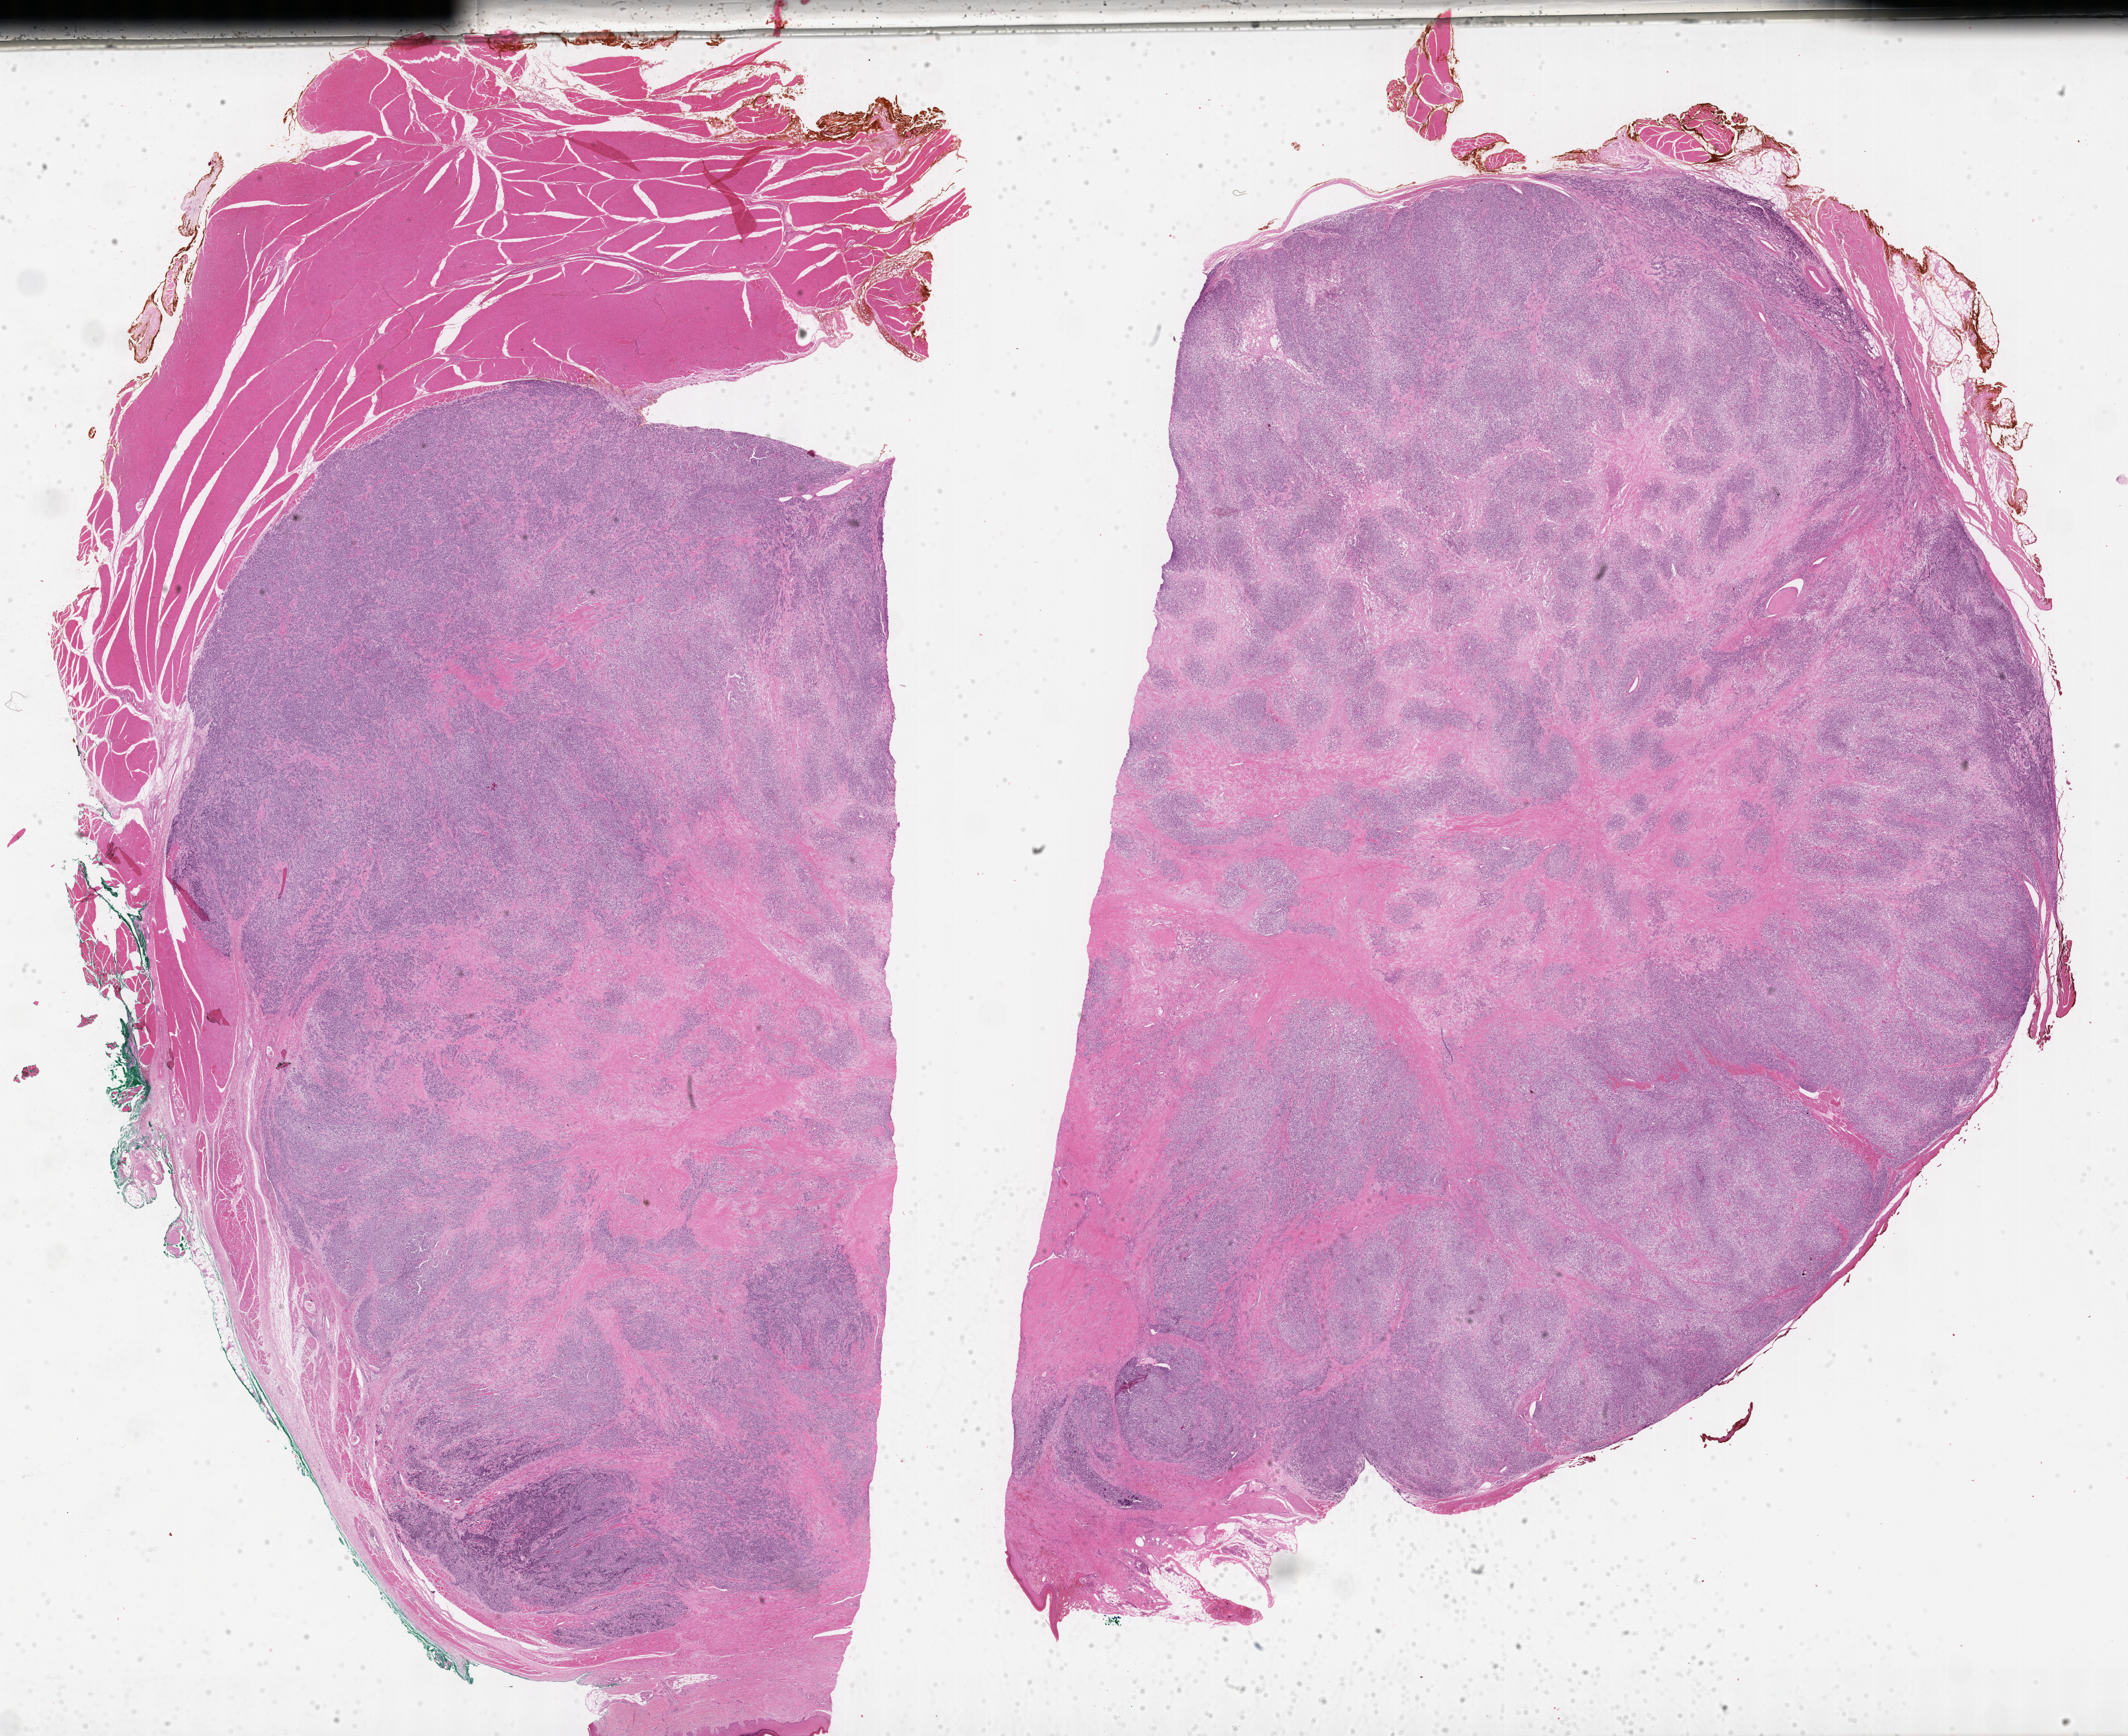
Whole-slide image, haematoxylin and eosin stain of tumor tissue, a low-resolution overview of the entire scanned area, about 29.2 x 23.8 mm, FFPE section, sample anatomic site: soft tissue, hand-right. Patient: male, age 11.2 years at diagnosis.
* metastatic status at presentation (as recorded): metastatic (confirmed)
* stage (as recorded): 4
* diagnosis: rhabdomyosarcoma; histological classification: alveolar rhabdomyosarcoma